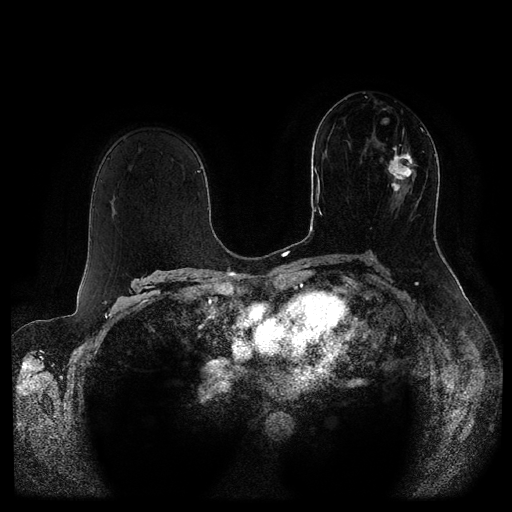
Breast MRI (dynamic contrast-enhanced, multi-phase), one axial slice. Position 56 of 116 along the scan axis. Dynamic contrast-enhanced series, time point 2 of 5 at this slice position (early post-contrast). 1.5 T. TE 2.6 ms, TR 5.3 ms. 2 mm slice thickness. 512 × 512 image matrix, field of view 370 × 370 mm. Female patient, age 51 years.
Outlined on this slice (semi-automatically segmented with operator editing):
- breast lesion (labelled 'tumour' in the annotation; benign lesions carry a separate 'benign' label): box from (x=379, y=128) to (x=418, y=192) px